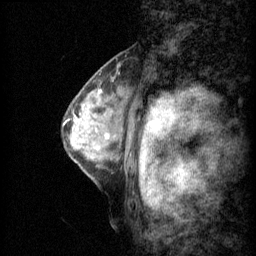
Breast MRI (dynamic contrast-enhanced), one sagittal slice. Position 41 of 60 along the scan axis. 3 images stored at this slice position (order not interpretable as contrast timing). 1.5 T. TE 4.2 ms, TR 11 ms. 1.5 mm slice thickness. 256 × 256 image matrix. Patient: female, 48 years.
Outlined on this slice (semi-automatically segmented with operator editing):
- analysis volume of interest (the breast-tissue region the enhancement analysis was run in; not a lesion): bounding box (x1, y1, x2, y2) in pixels: (62, 76, 128, 143)
- tumour enhancement mask (voxels above the 70 % enhancement threshold inside the analysis volume of interest): (98, 90, 101, 93)